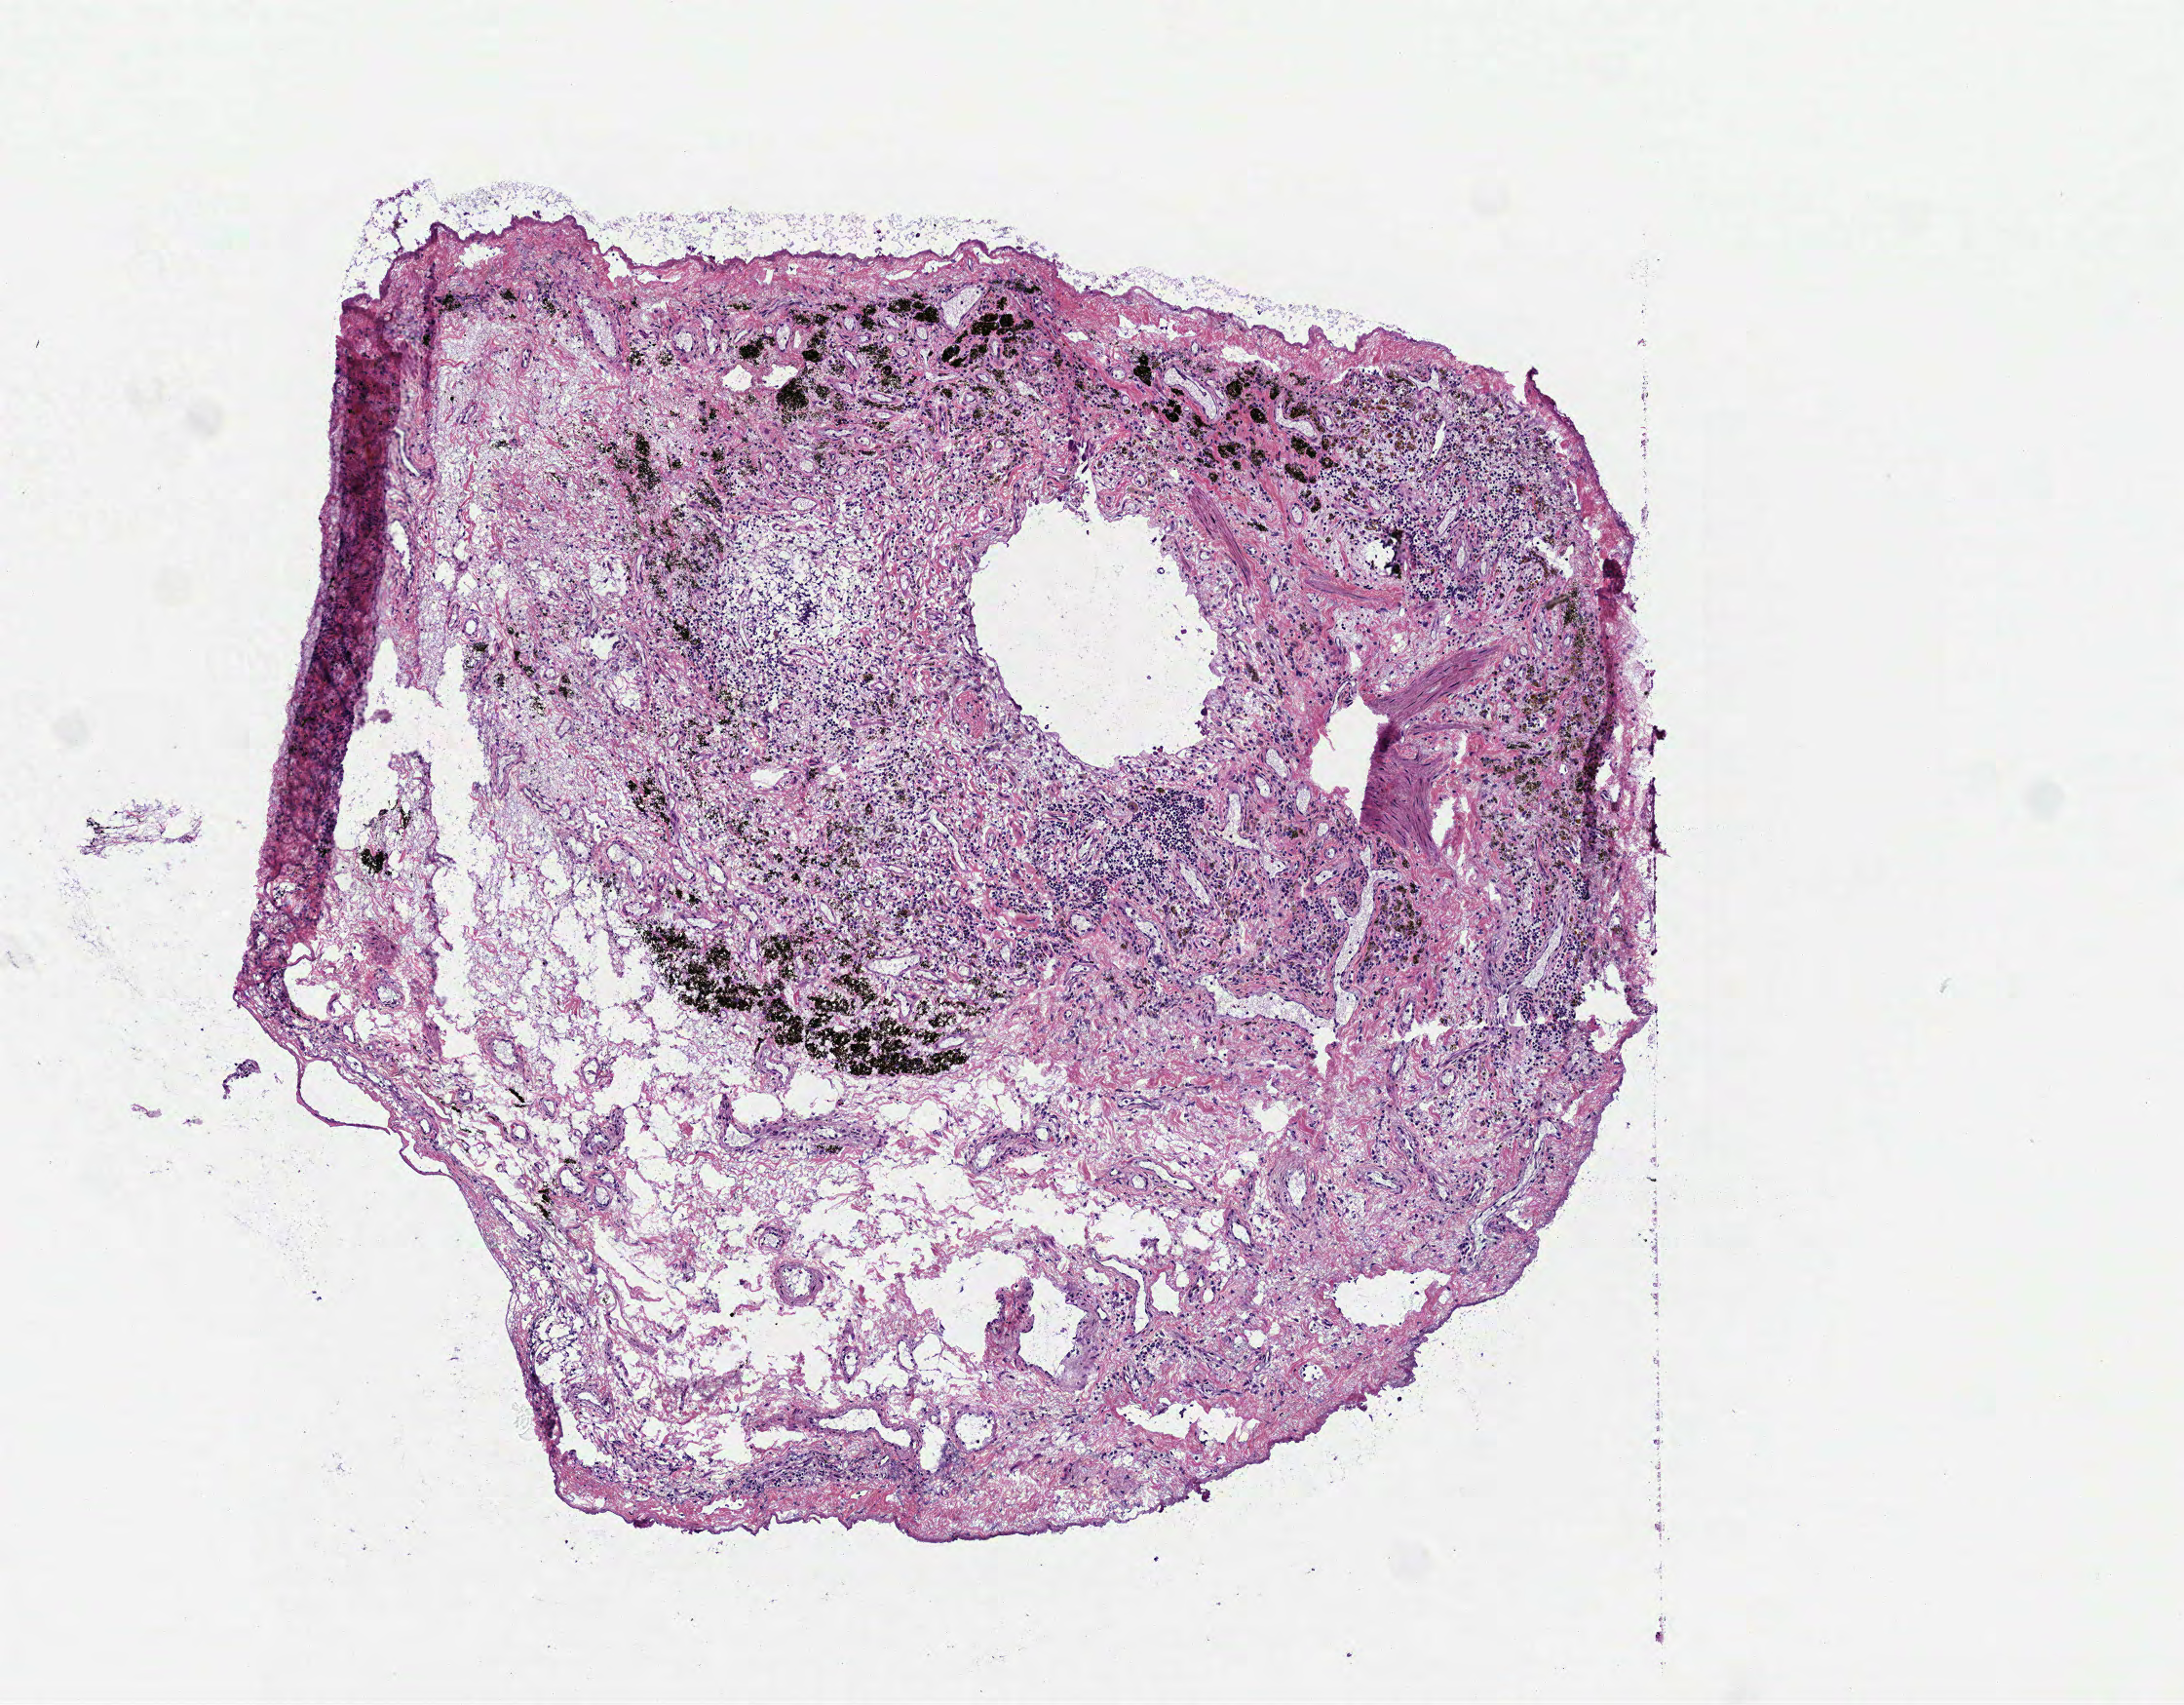
Hematoxylin and eosin (H&E) stained whole-slide image — a low-resolution overview of the entire scanned area, about 4.5 x 3.5 mm (slide scanned at 40x); frozen section; solid tissue normal (non-tumour tissue) sample from the lung. Male patient; age at initial diagnosis 70 years. Inflammatory infiltration, as recorded: lymphocyte infiltration 15%, monocyte infiltration 5%, neutrophil infiltration 0%.
This section: solid tissue normal sample (biorepository sample class). Patient diagnosis: Squamous cell carcinoma, NOS.